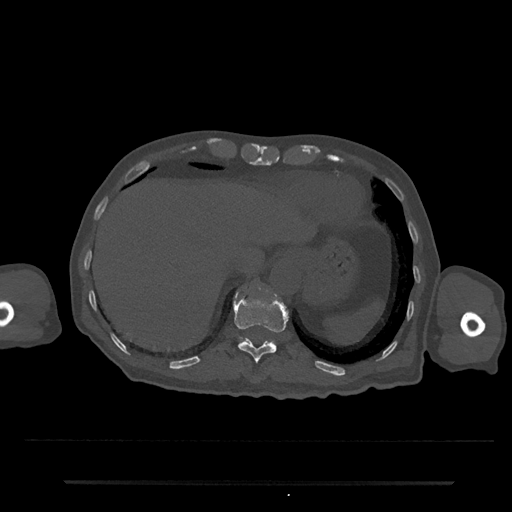
CT including the spine, one axial slice; slice 248 of 797 in the series (ordered by position); reconstruction kernel Br40s/3; 120 kVp; bone window (W 1800 / L 400 HU); 0.5 mm slice thickness; 512 × 512 image matrix, field of view 427 × 427 mm. Patient: male, 74 years. Case-level facts recorded for this patient, not image findings: primary cancer: prostate.
Structures marked on this image (semi-automatically segmented with operator editing):
- T10 vertebra: bounding box <254,380,258,382> (left, top, right, bottom; pixels)
- T11 vertebra: <233,290,288,363>